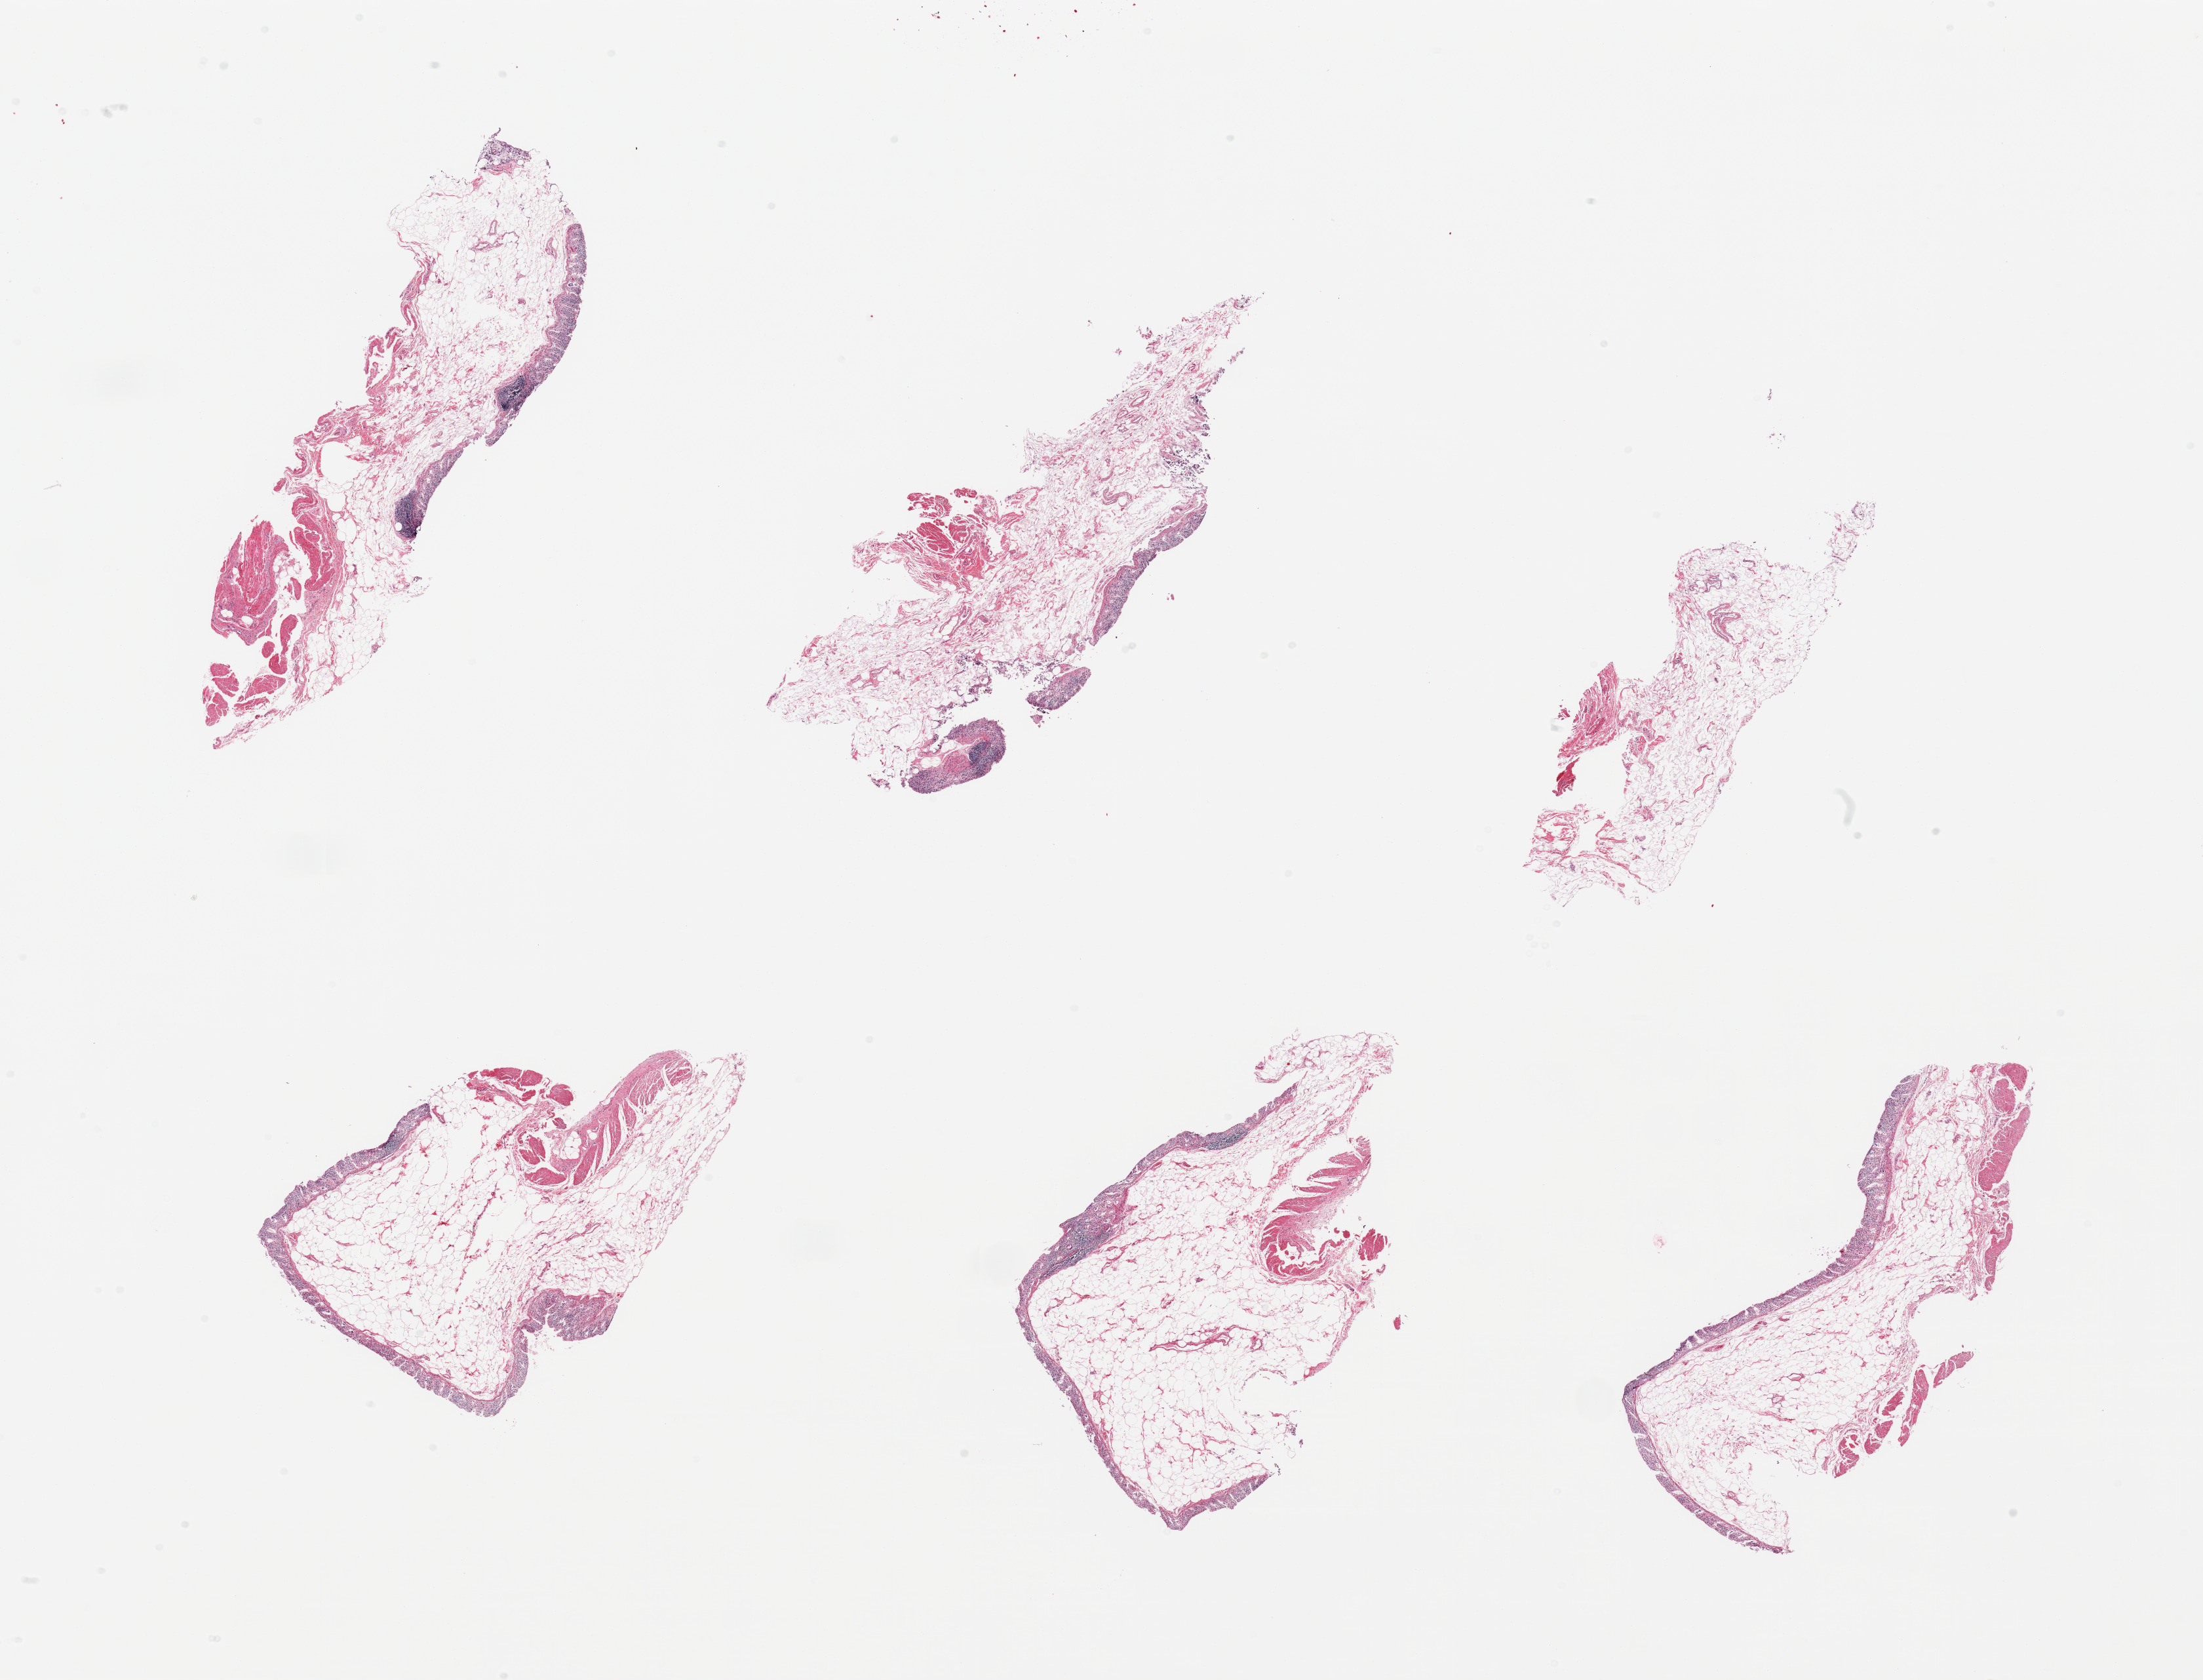
Haematoxylin and eosin whole-slide image, a low-resolution overview of the entire scanned area, about 26.6 x 20.3 mm (acquisition: 20x scan). PAXgene-fixed, paraffin-embedded tissue. Sampled site (target tissue): transverse colon. Tissue donor sample. Donor: male.
Reviewer comment on this tissue sample: 6 pieces; autolyzed mucosa with a few scattered lymphoid aggregates and trace of preserved muscularis, largely fat/submucosa.